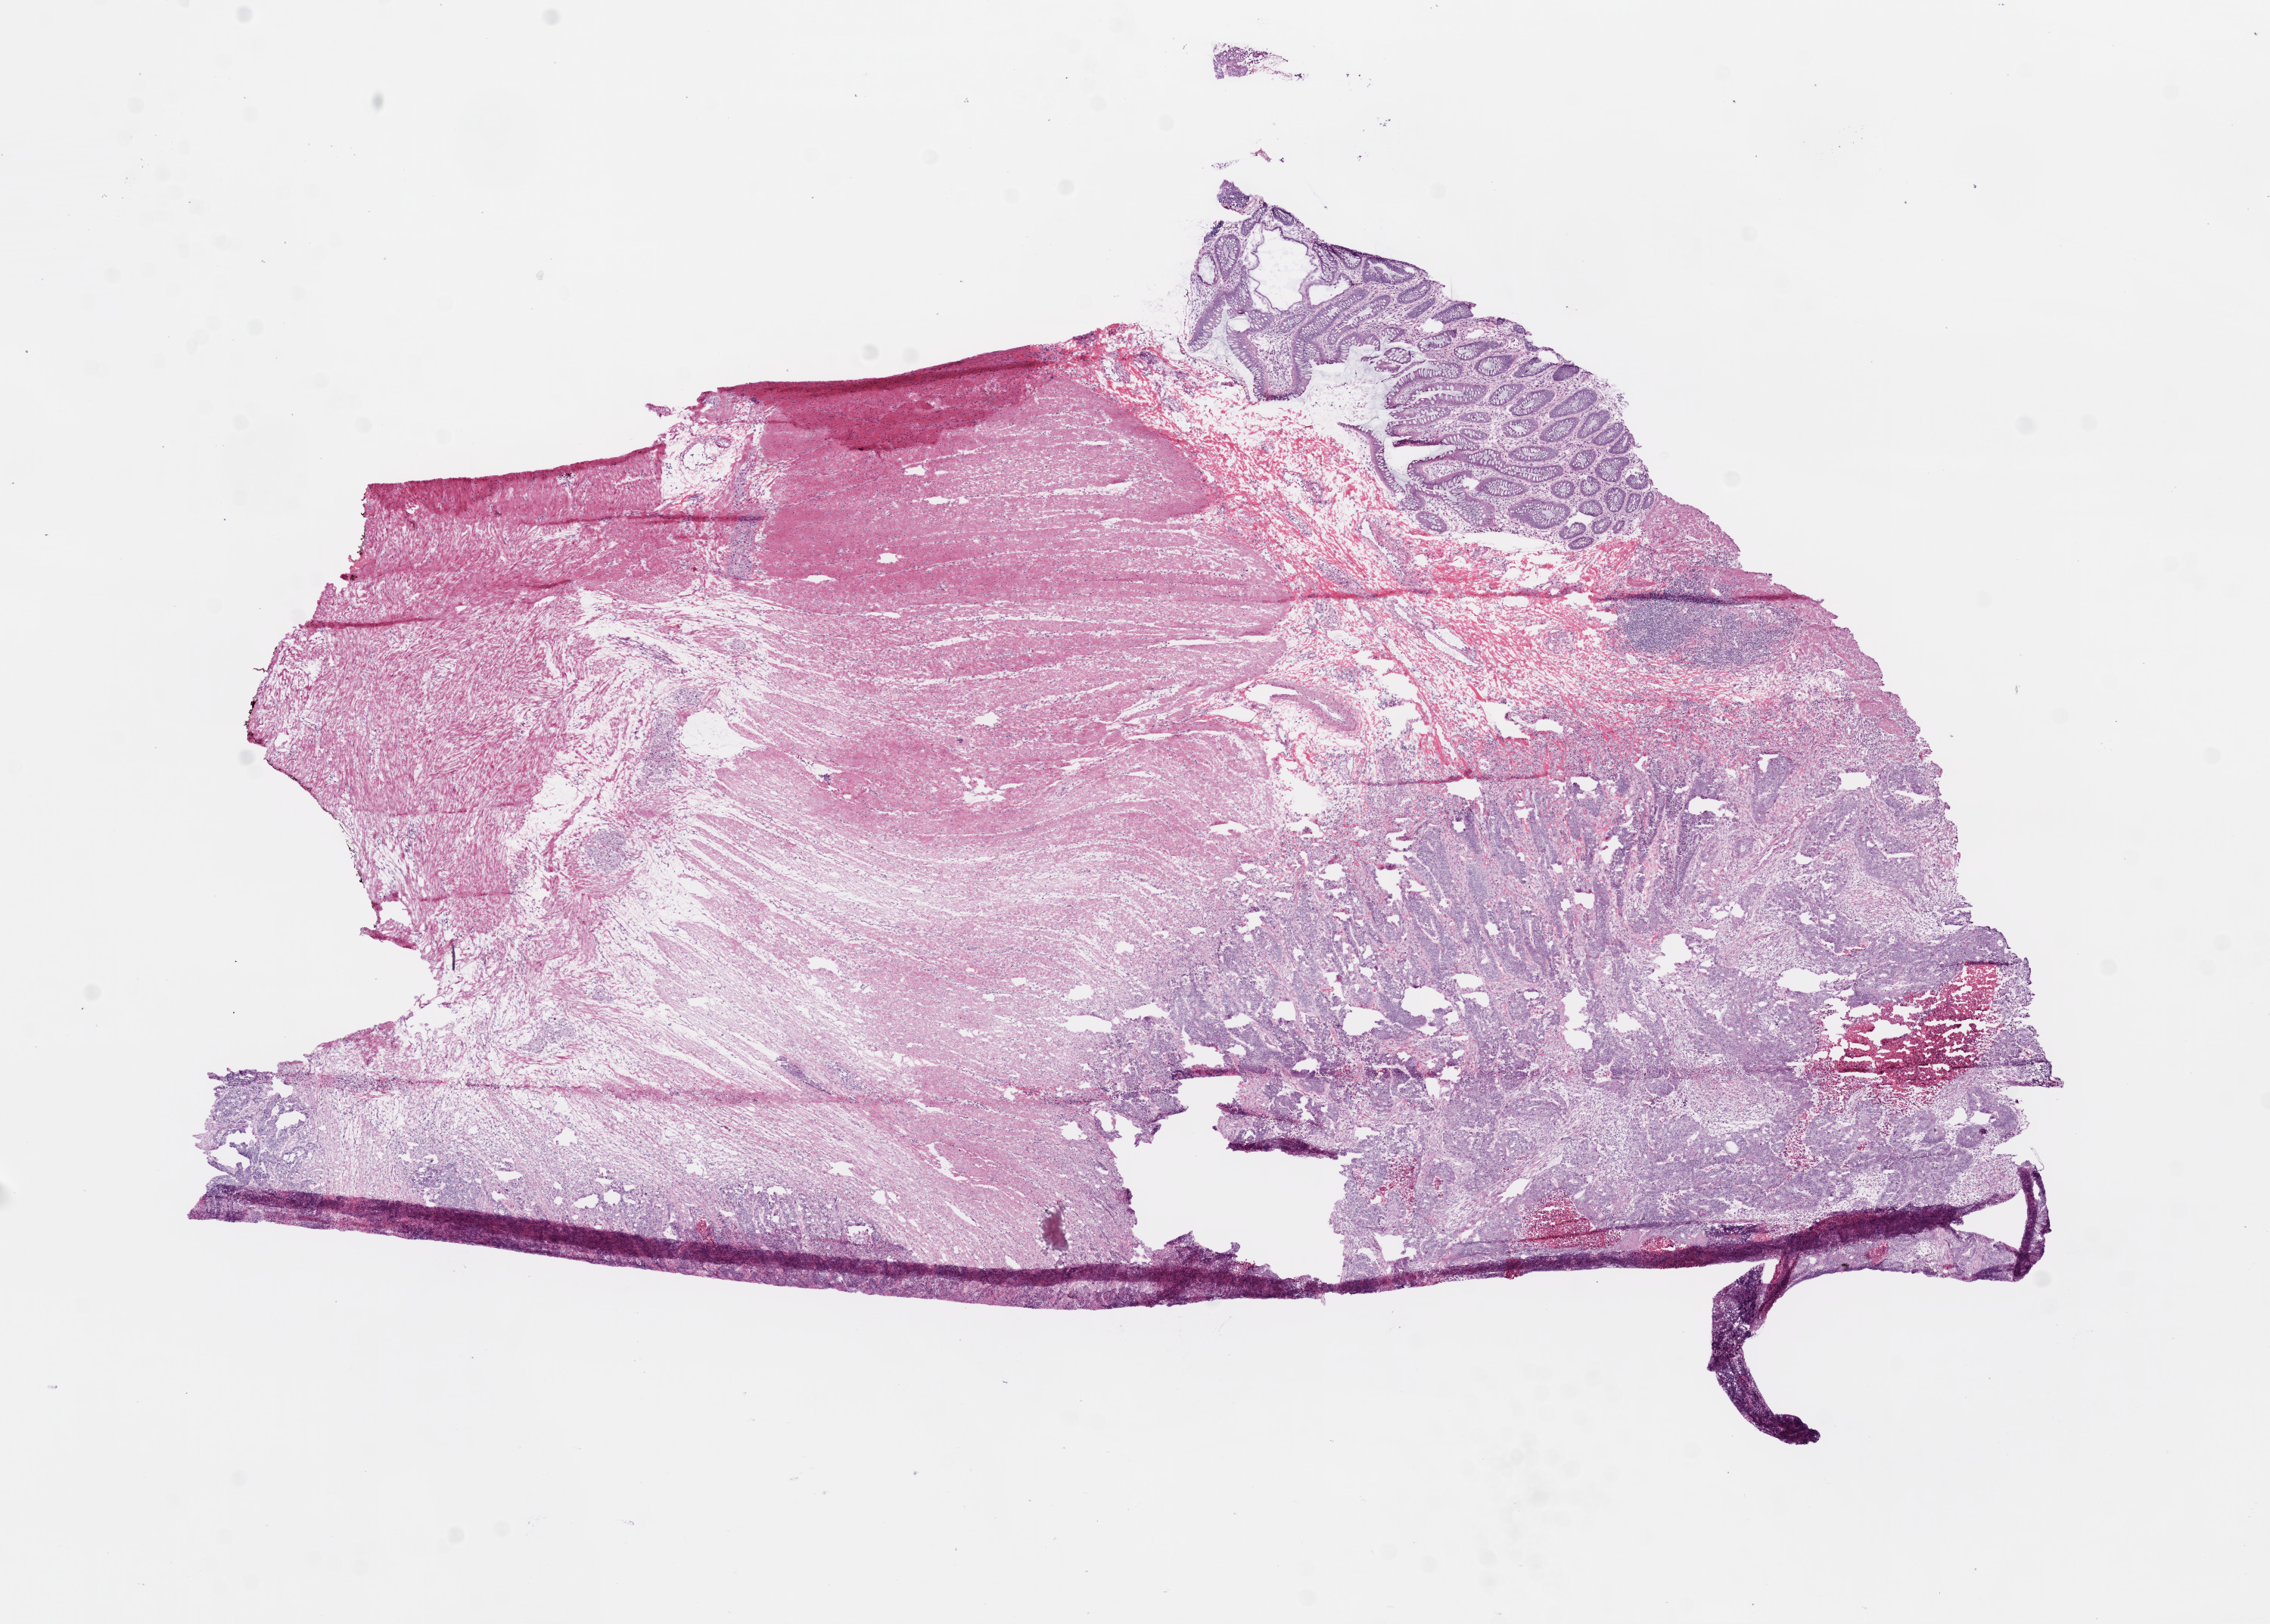
H&E whole-slide image — low-resolution overview of the scanned area, about 12.0 x 8.6 mm. Frozen section. Rectum, primary tumour sample. Male, age 48 years at initial diagnosis. Pathologist review of this section (percent, as recorded): tumour cells 20%, tumour nuclei 50%, normal cells 70%, stromal cells 5%, necrosis 5%.
- histologic diagnosis: Adenocarcinoma, NOS
- AJCC pathologic stage: IIIC (6th edition)
- lymph nodes positive (case pathology): 9 of 18 examined